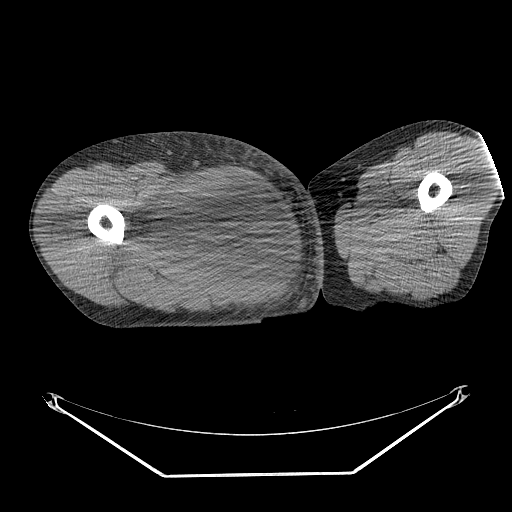
CT of an extremity soft-tissue mass (from a PET/CT study), one axial slice. Position 251 of 311 along the scan axis. Reconstruction kernel STANDARD. 140 kVp. Soft-tissue window (W 400 / L 40 HU). 3.75 mm slice thickness. 512 × 512 image matrix. Male patient. From the clinical record (not read from this slice): histological type: undifferentiated - pleiomorphic; grade: high; site of the primary tumour: right thigh.
Structures marked on this image (expert contour drawn on MRI and transferred to this co-registered scan by the dataset authors):
- gross tumour volume including surrounding oedema: box from (x=135, y=173) to (x=257, y=266) px
- gross tumour volume (mass): (x=155, y=174)–(x=257, y=266)